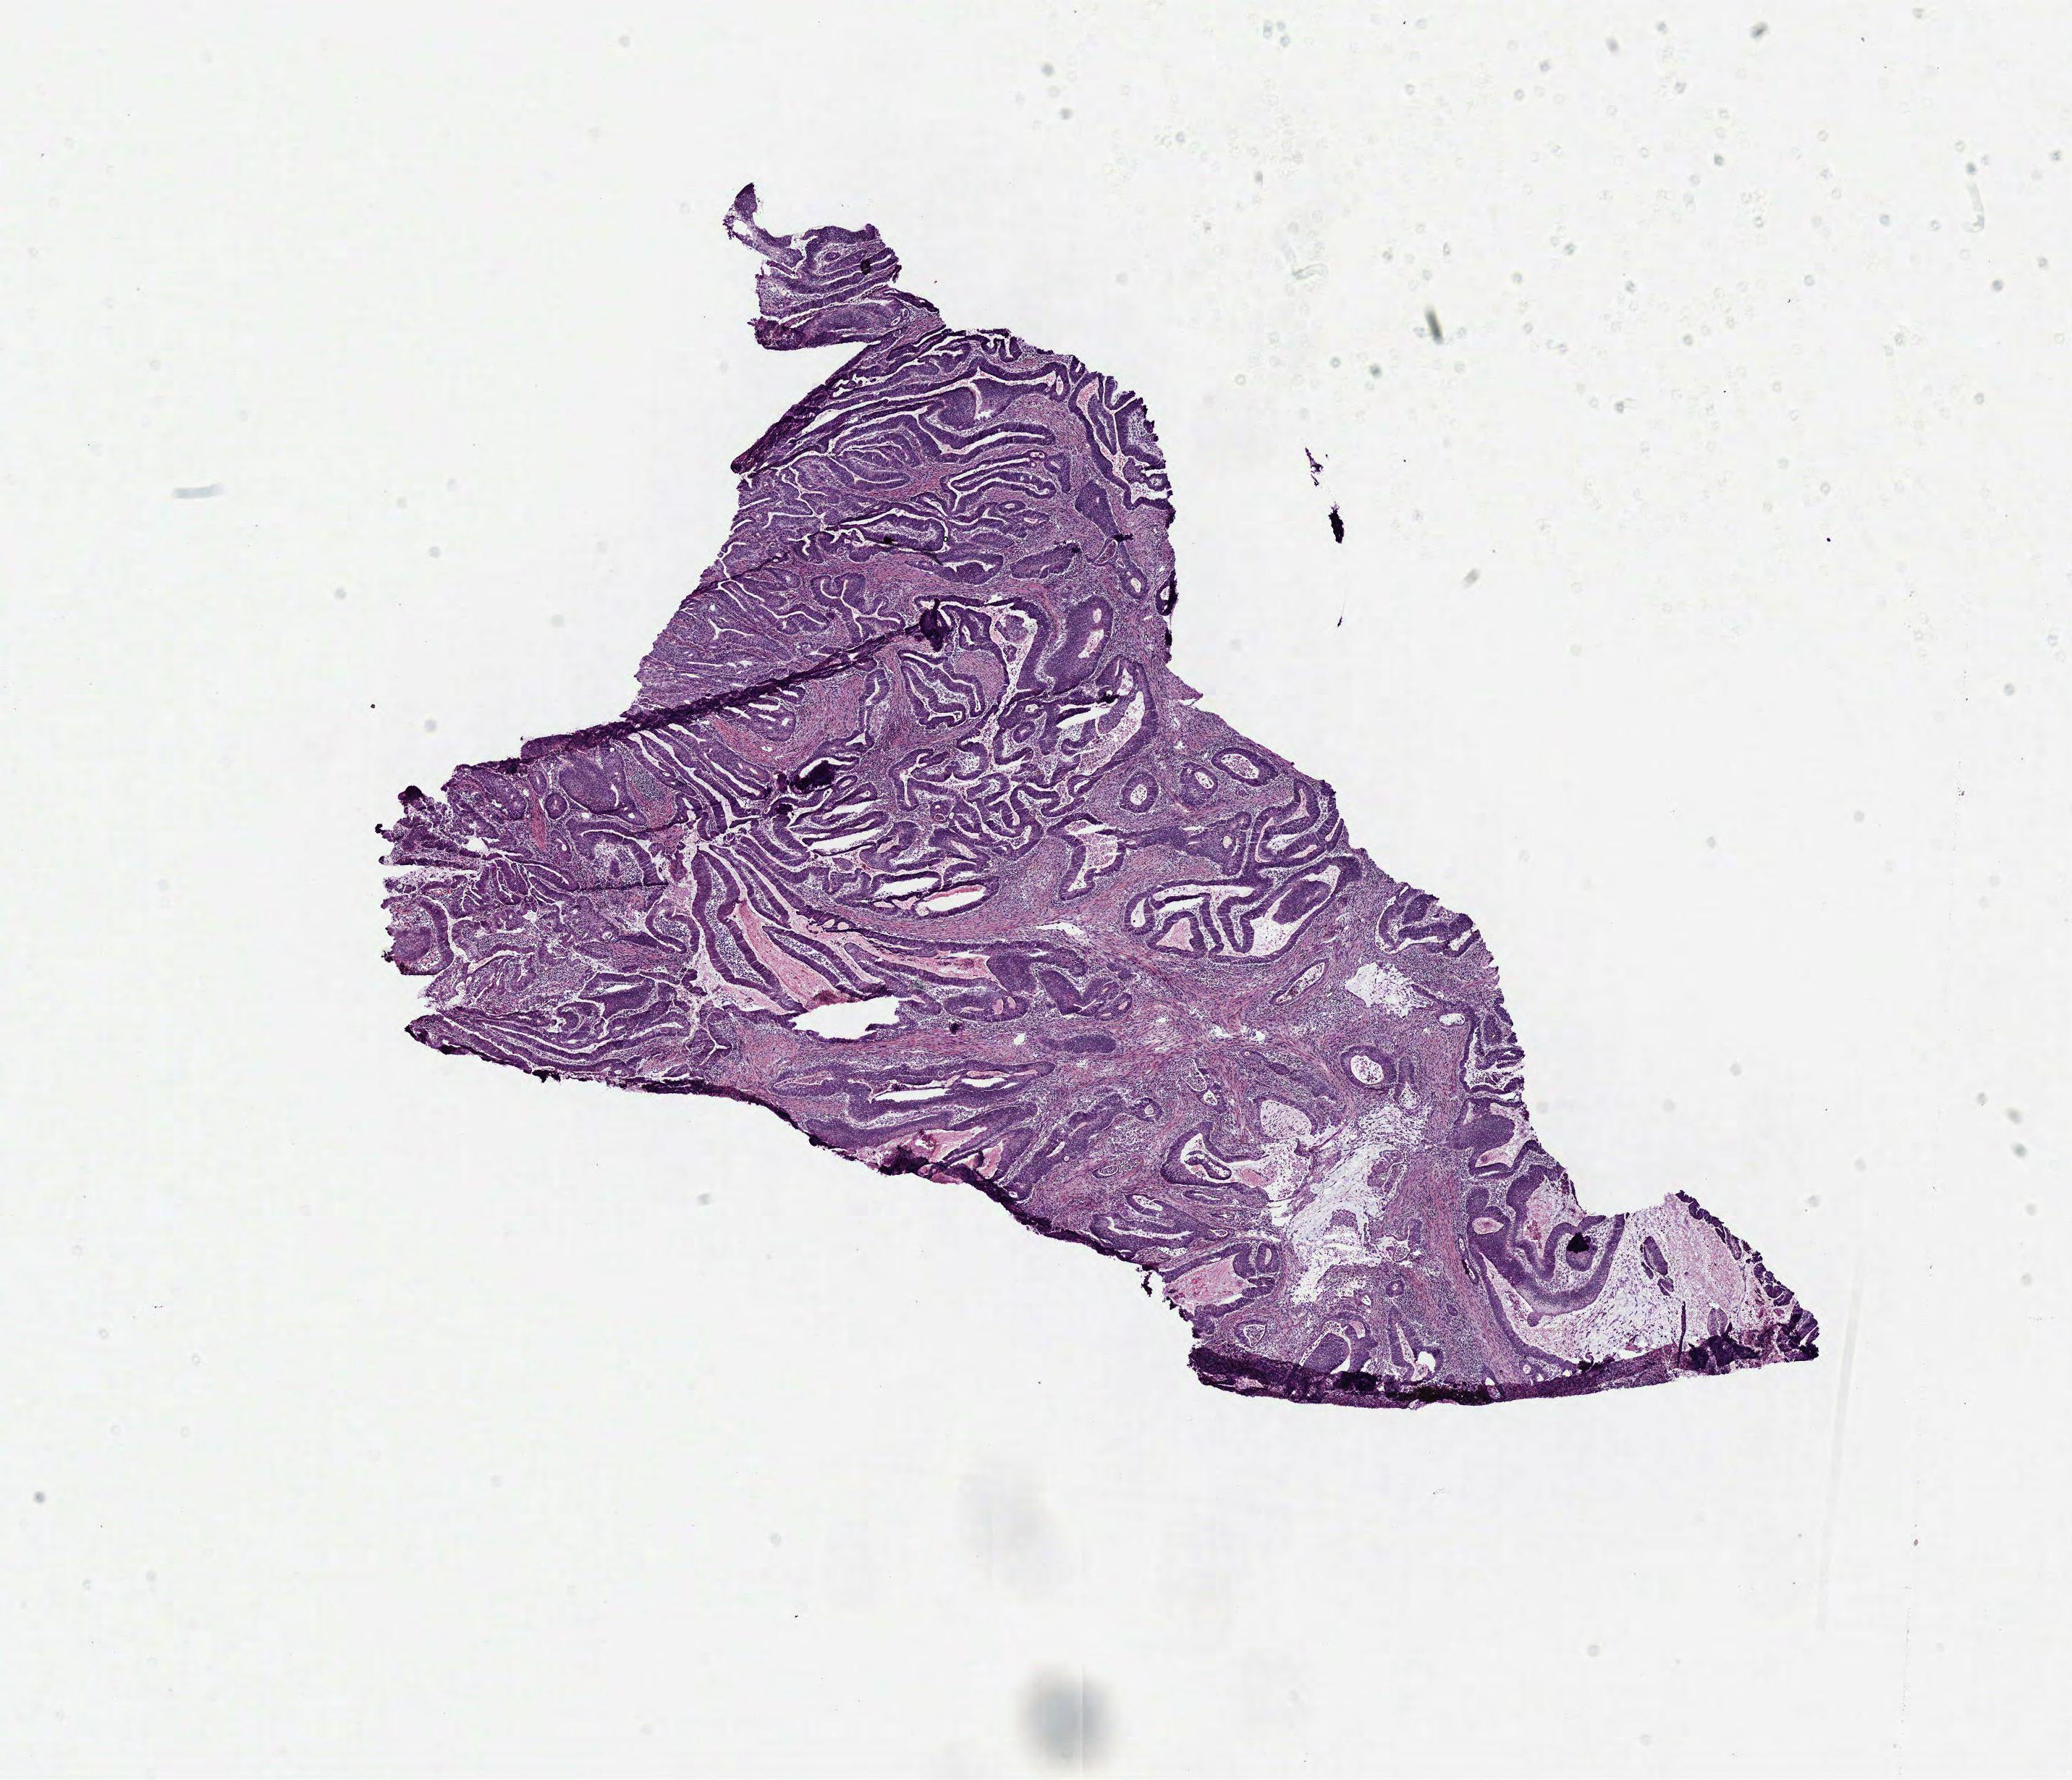
Whole-slide histology image, H&E, low-resolution overview of the scanned area, about 11.3 x 9.7 mm, frozen section, sample: primary tumour, colon. Patient: female, age at initial diagnosis 49 years. Pathologist review of this section (percent, as recorded): tumour cells 80%, tumour nuclei 80%, normal cells 0%, stromal cells 20%, necrosis 0%.
Diagnosis: Adenocarcinoma, NOS. AJCC pathologic stage: III (5th edition). Lymph nodes positive (case pathology): 1 of 26 examined.